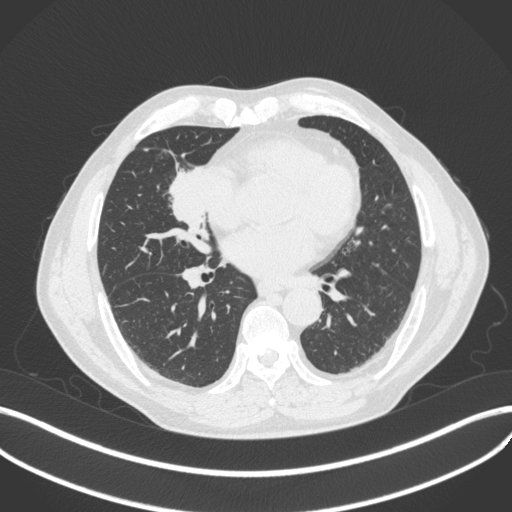
Chest CT, one axial slice; position 181 of 429 along the scan axis; 120 kVp; lung window (W 1500 / L -600 HU); 1 mm slice thickness; 512 × 512 image matrix, field of view 400 × 400 mm. Male patient, age 61 years. Case-level facts recorded for this patient, not image findings: clinical TNM (as recorded): T2b N1 M0.
Annotated regions visible in this slice (bounding box drawn by a radiologist):
- lung tumour (recorded histology: squamous cell carcinoma): bounding box <160,152,222,231> (left, top, right, bottom; pixels)